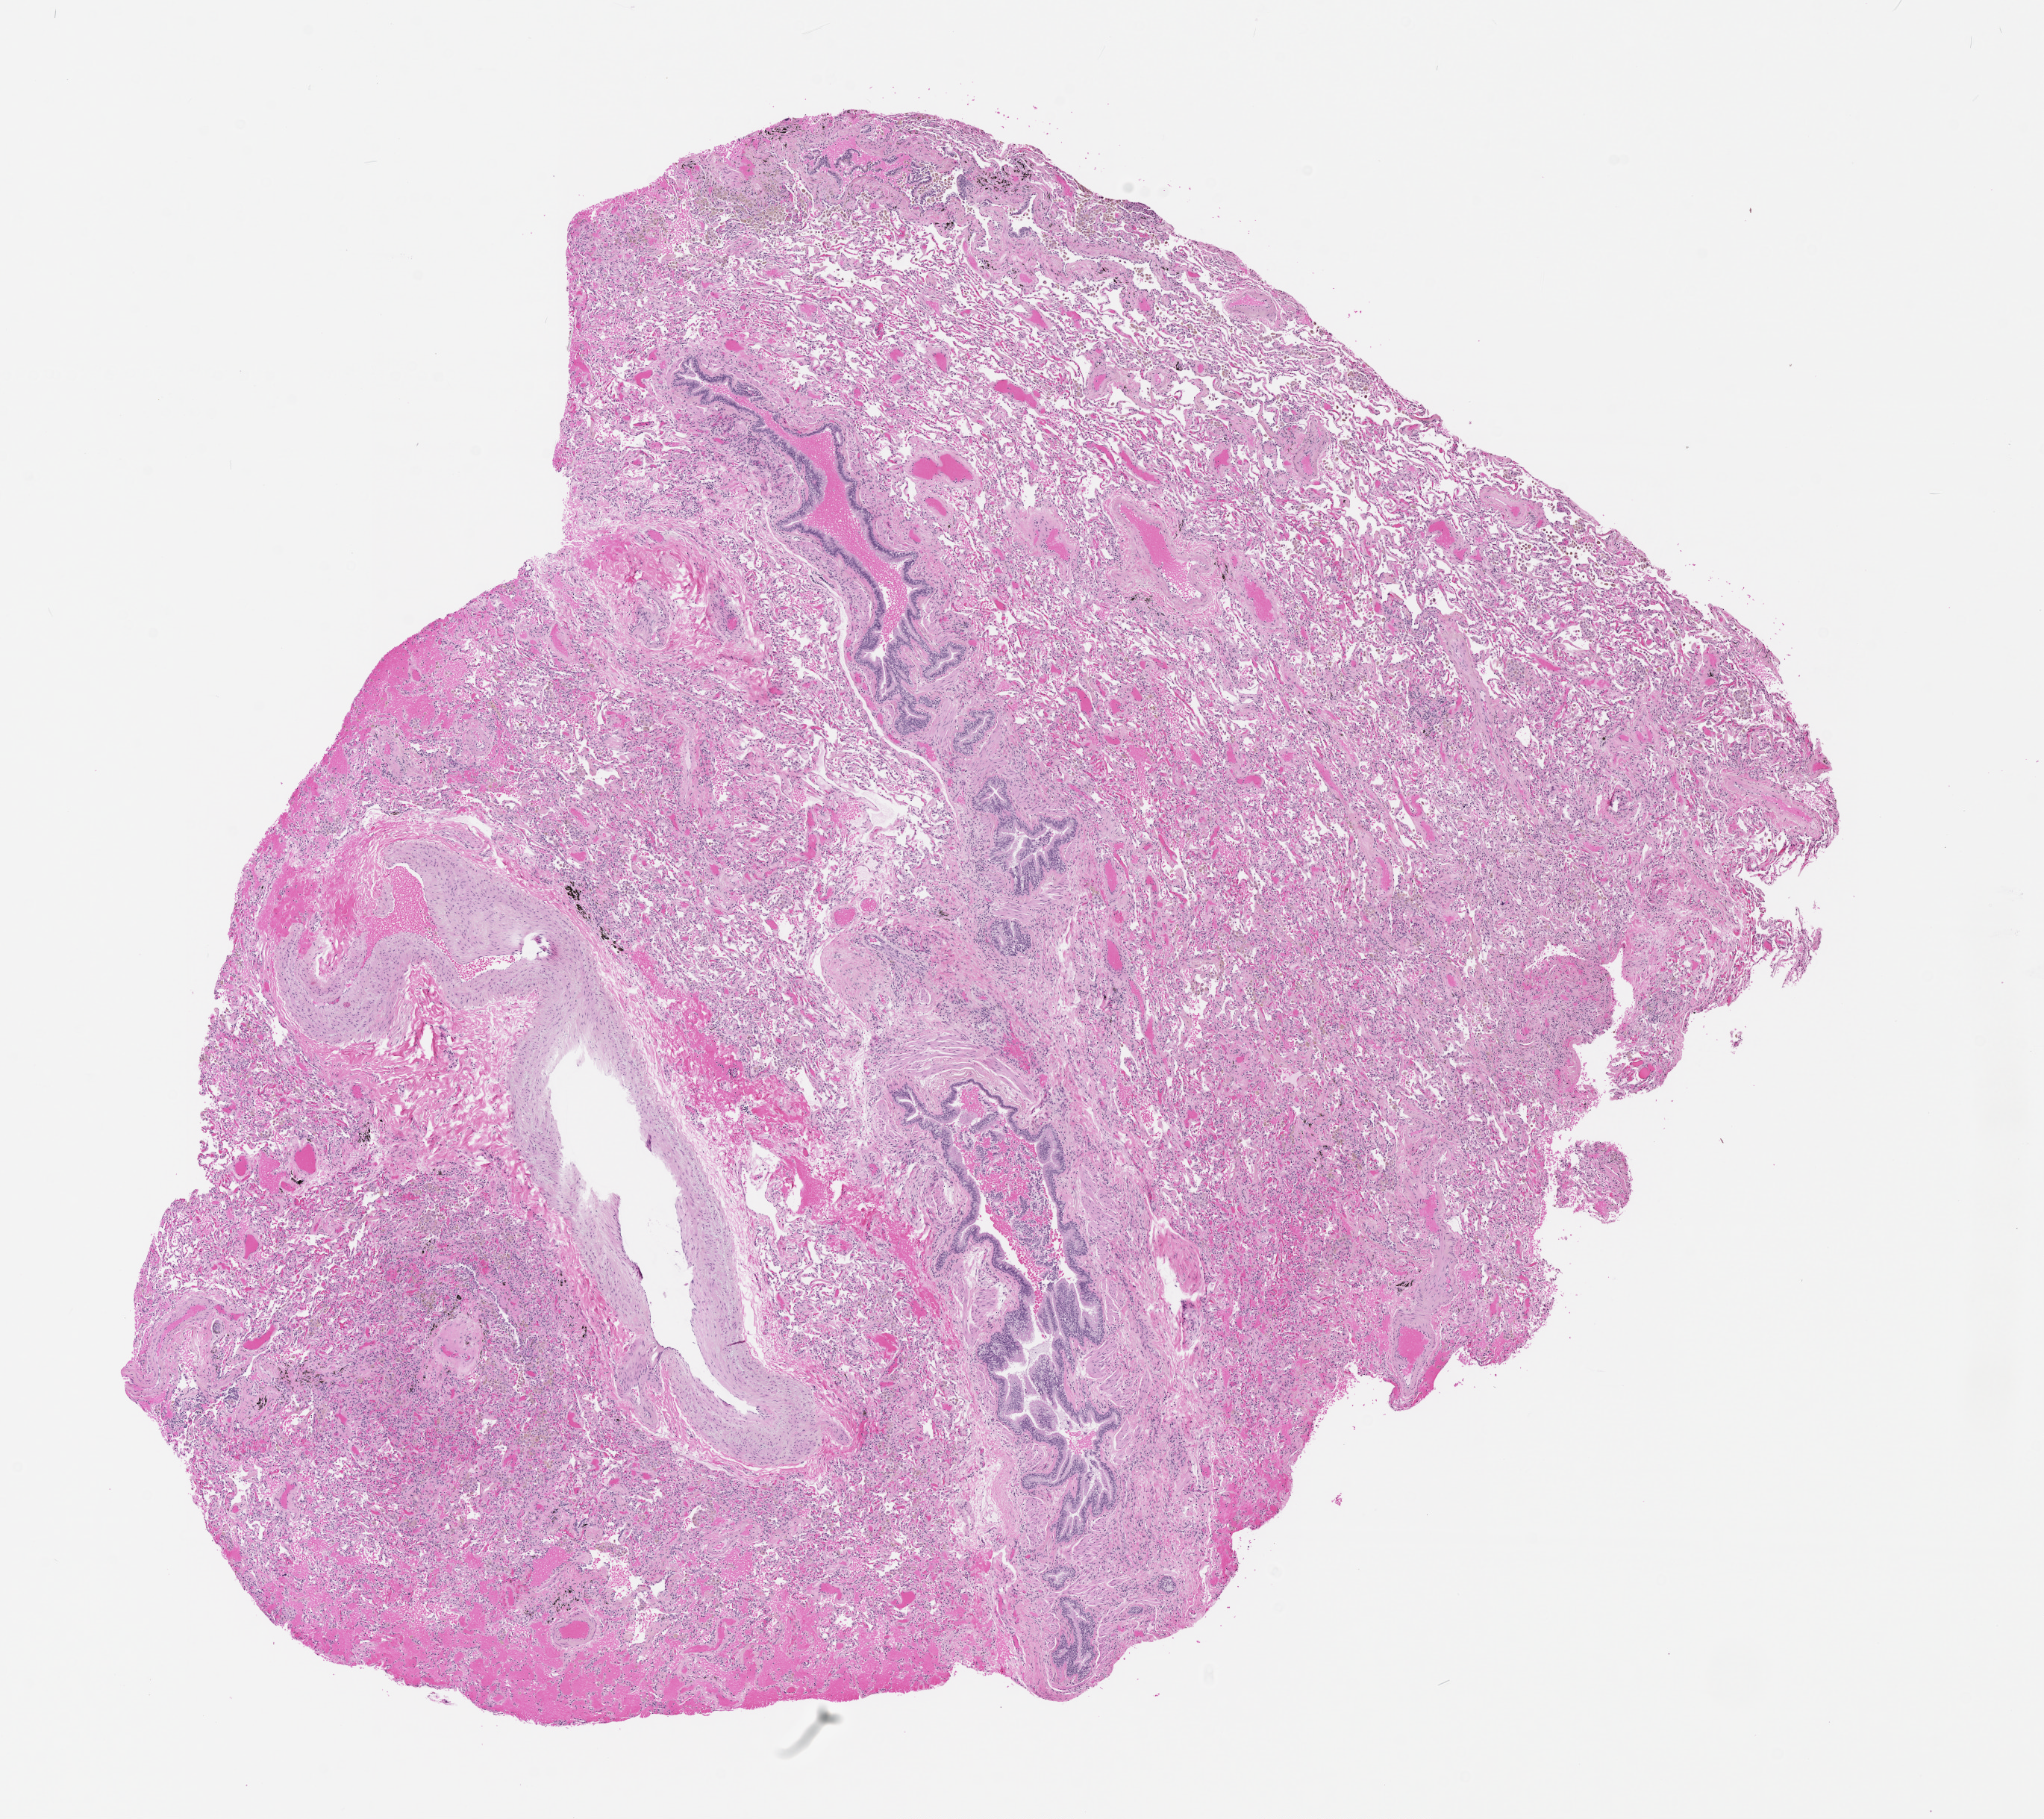
Whole-slide histology image, Hematoxylin and eosin (H&E) stained, low-resolution overview of the scanned area, about 11.0 x 9.8 mm; lung, tissue type not recorded.
• patient diagnosis (cohort enrolment): squamous cell carcinoma (lung)